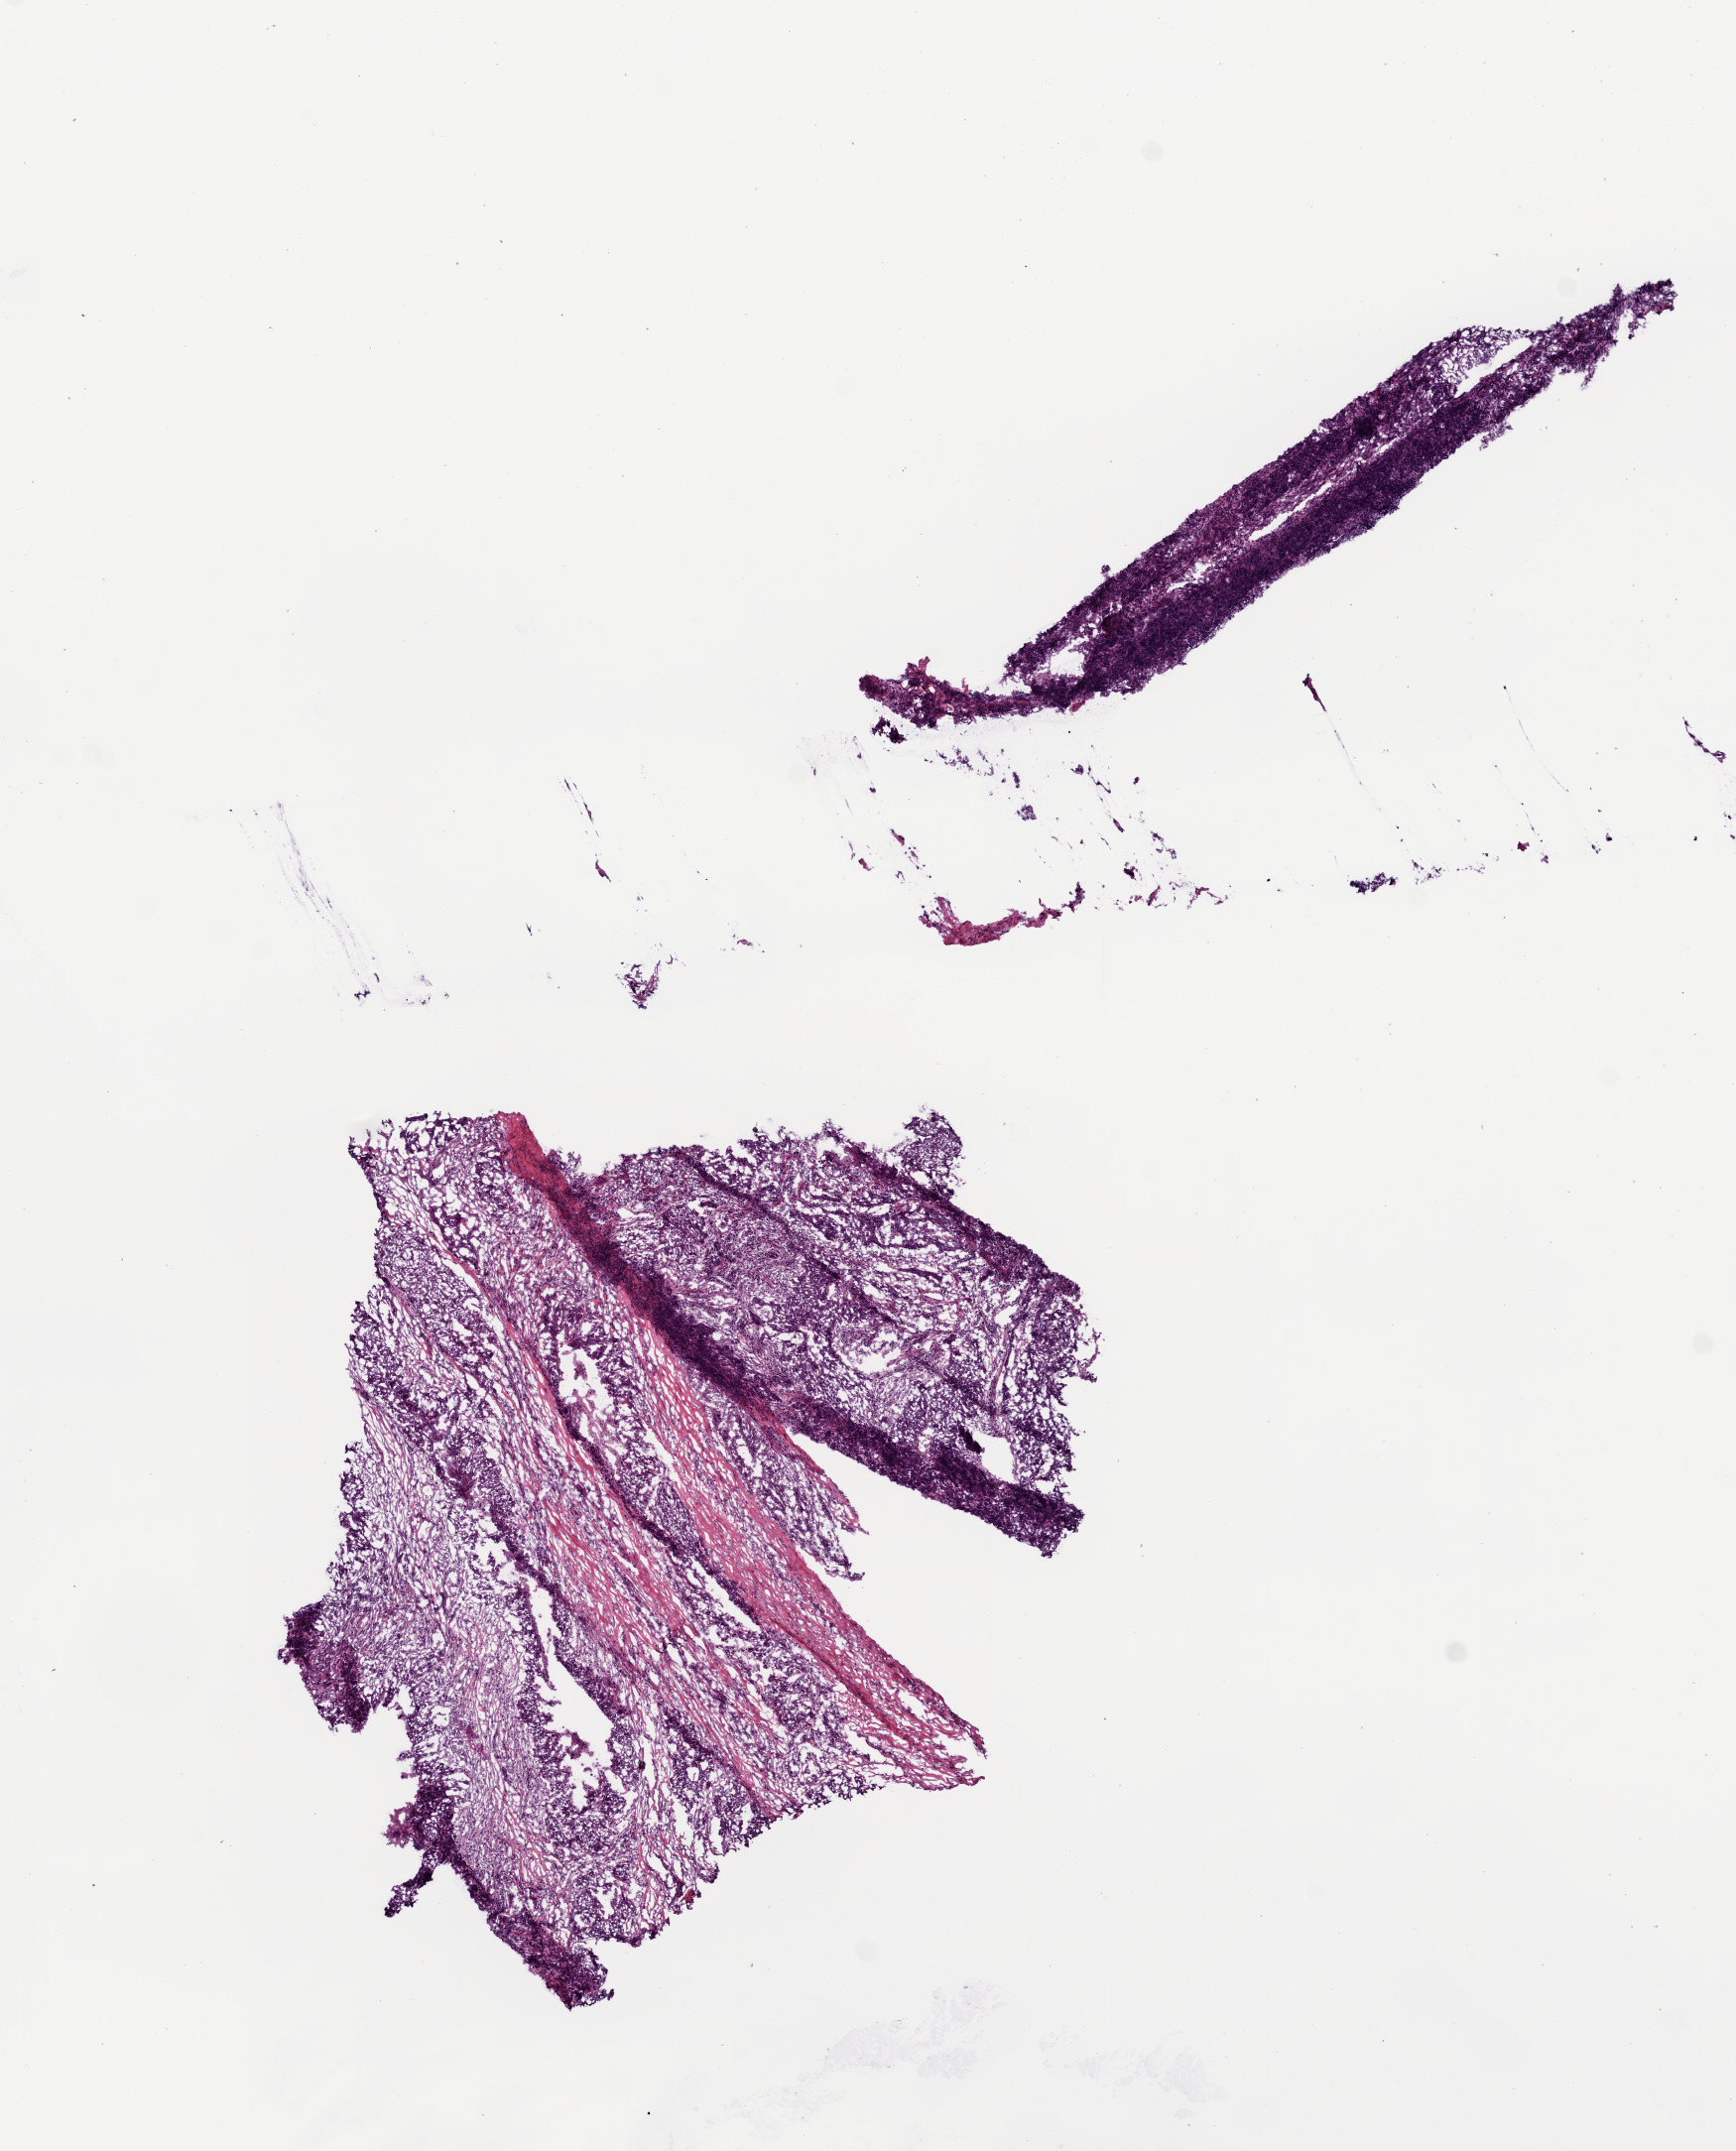
Digitized H&E tissue section (whole slide), whole scanned area (about 7.0 x 8.7 mm) shown as a low-resolution overview. Frozen section from the bottom of the tissue portion. Head and neck, primary tumour sample. Male, age 73 years at initial diagnosis. Histologic grade: G3 (poorly differentiated). Pathologist review of this section (percent, as recorded): tumour cells 50%, tumour nuclei 60%, normal cells 0%, stromal cells 50%, necrosis 0%.
AJCC pathologic stage: IVA (7th edition). Pathologic diagnosis: Squamous cell carcinoma, NOS (larynx, NOS).